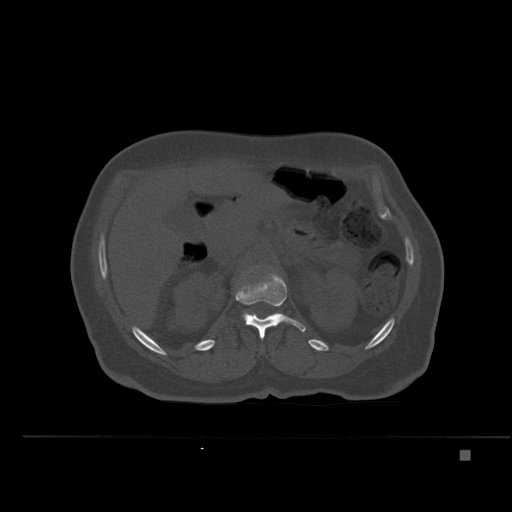
CT including the spine, one axial slice. Position 233 of 477 along the scan axis. Bone window (W 1800 / L 400 HU). 1.5 mm slice thickness. 512 × 512 image matrix, field of view 422 × 422 mm. Patient: female, 74 years. Case-level facts recorded for this patient, not image findings: primary cancer: colon.
Annotated regions visible in this slice (semi-automatically segmented with operator editing):
- L1 vertebra: bounding box <235,273,306,339> (left, top, right, bottom; pixels)